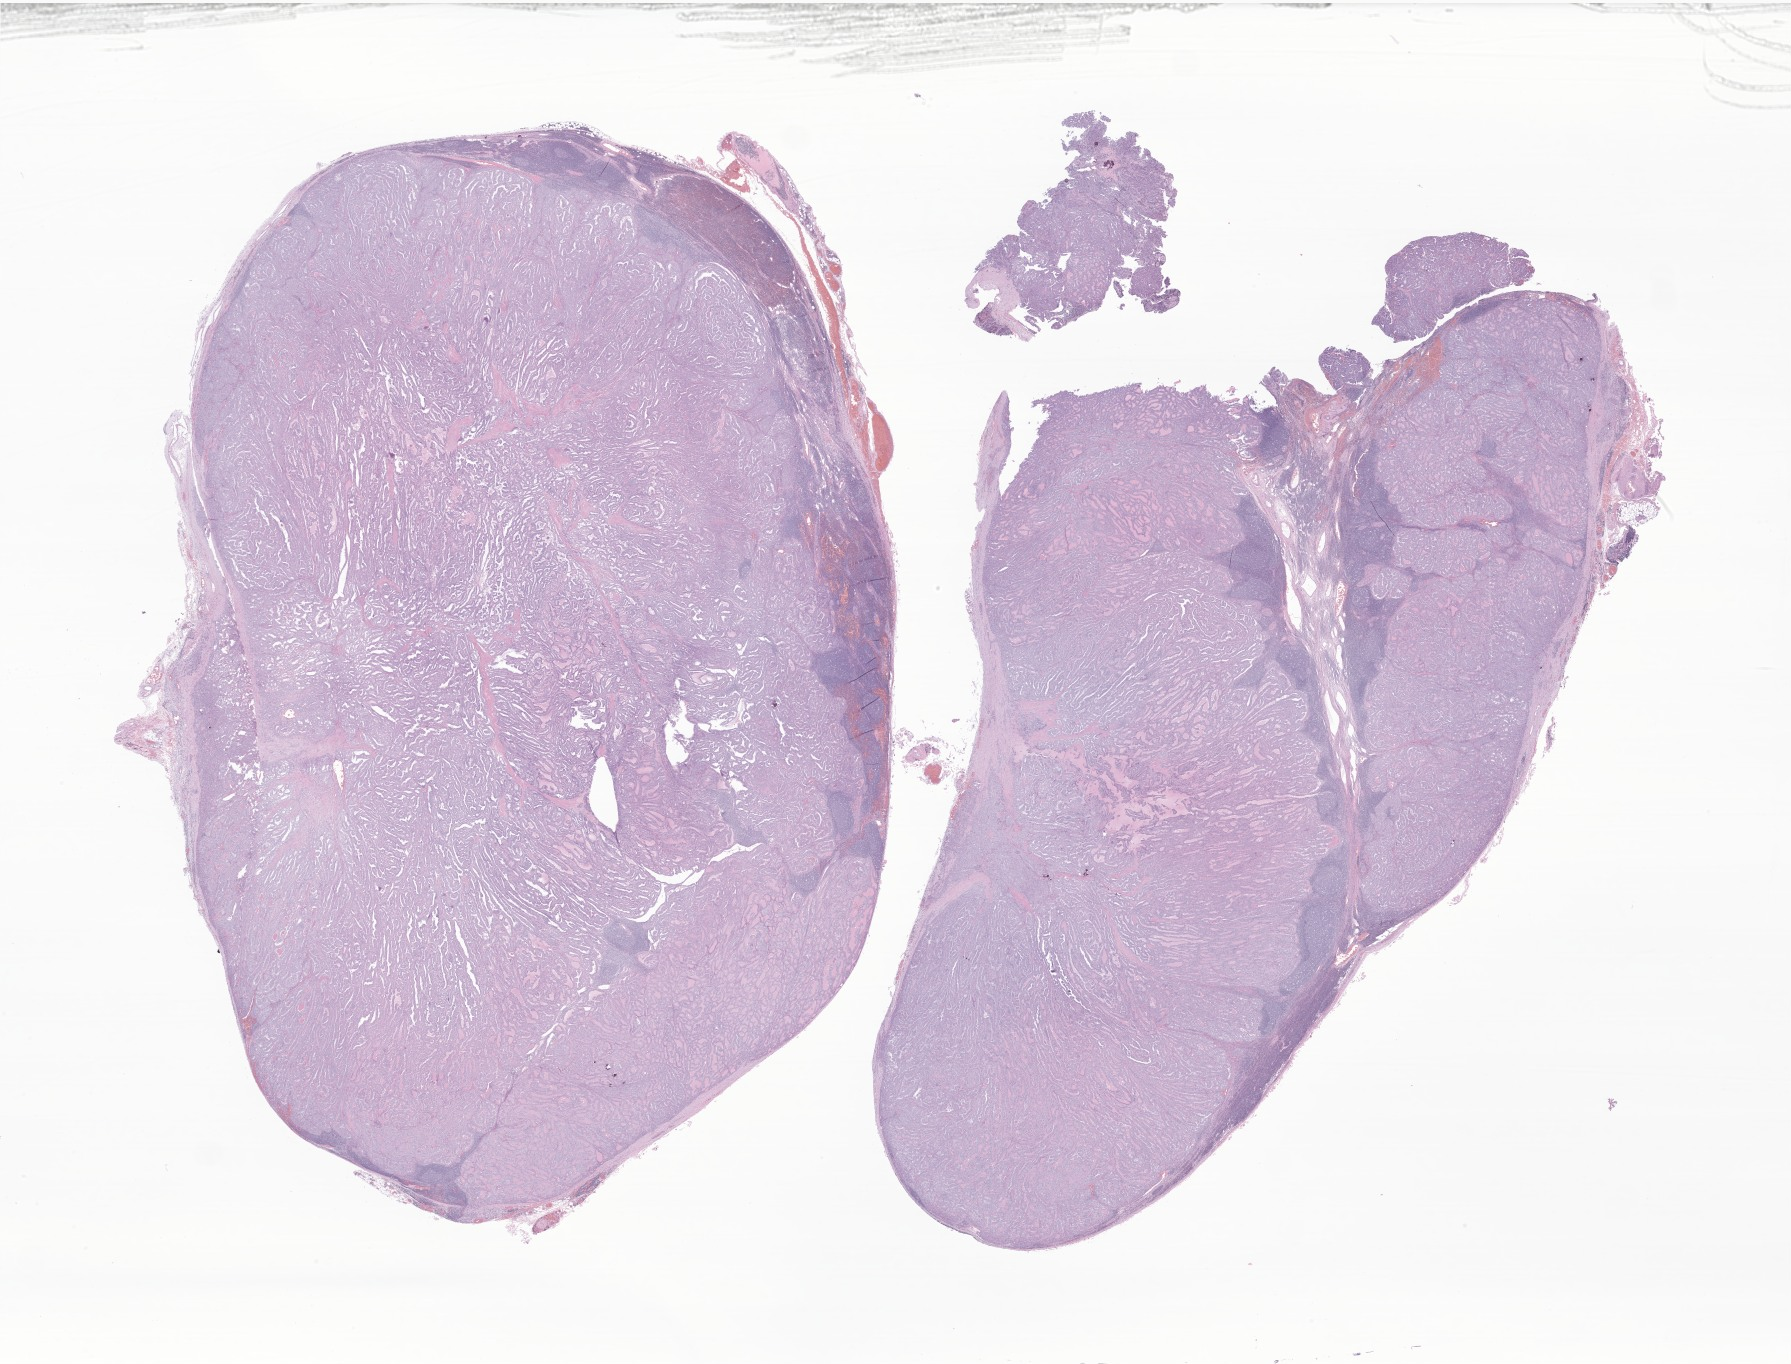
Whole-slide image, hematoxylin and eosin (H&E) stain of tumor tissue from the thyroid, whole scanned area (about 30.2 x 23.0 mm) shown as a low-resolution overview. Formalin-fixed paraffin-embedded section. Female patient, age 165 months (13 years 9 months).
Diagnosis: Papillary carcinoma, NOS.